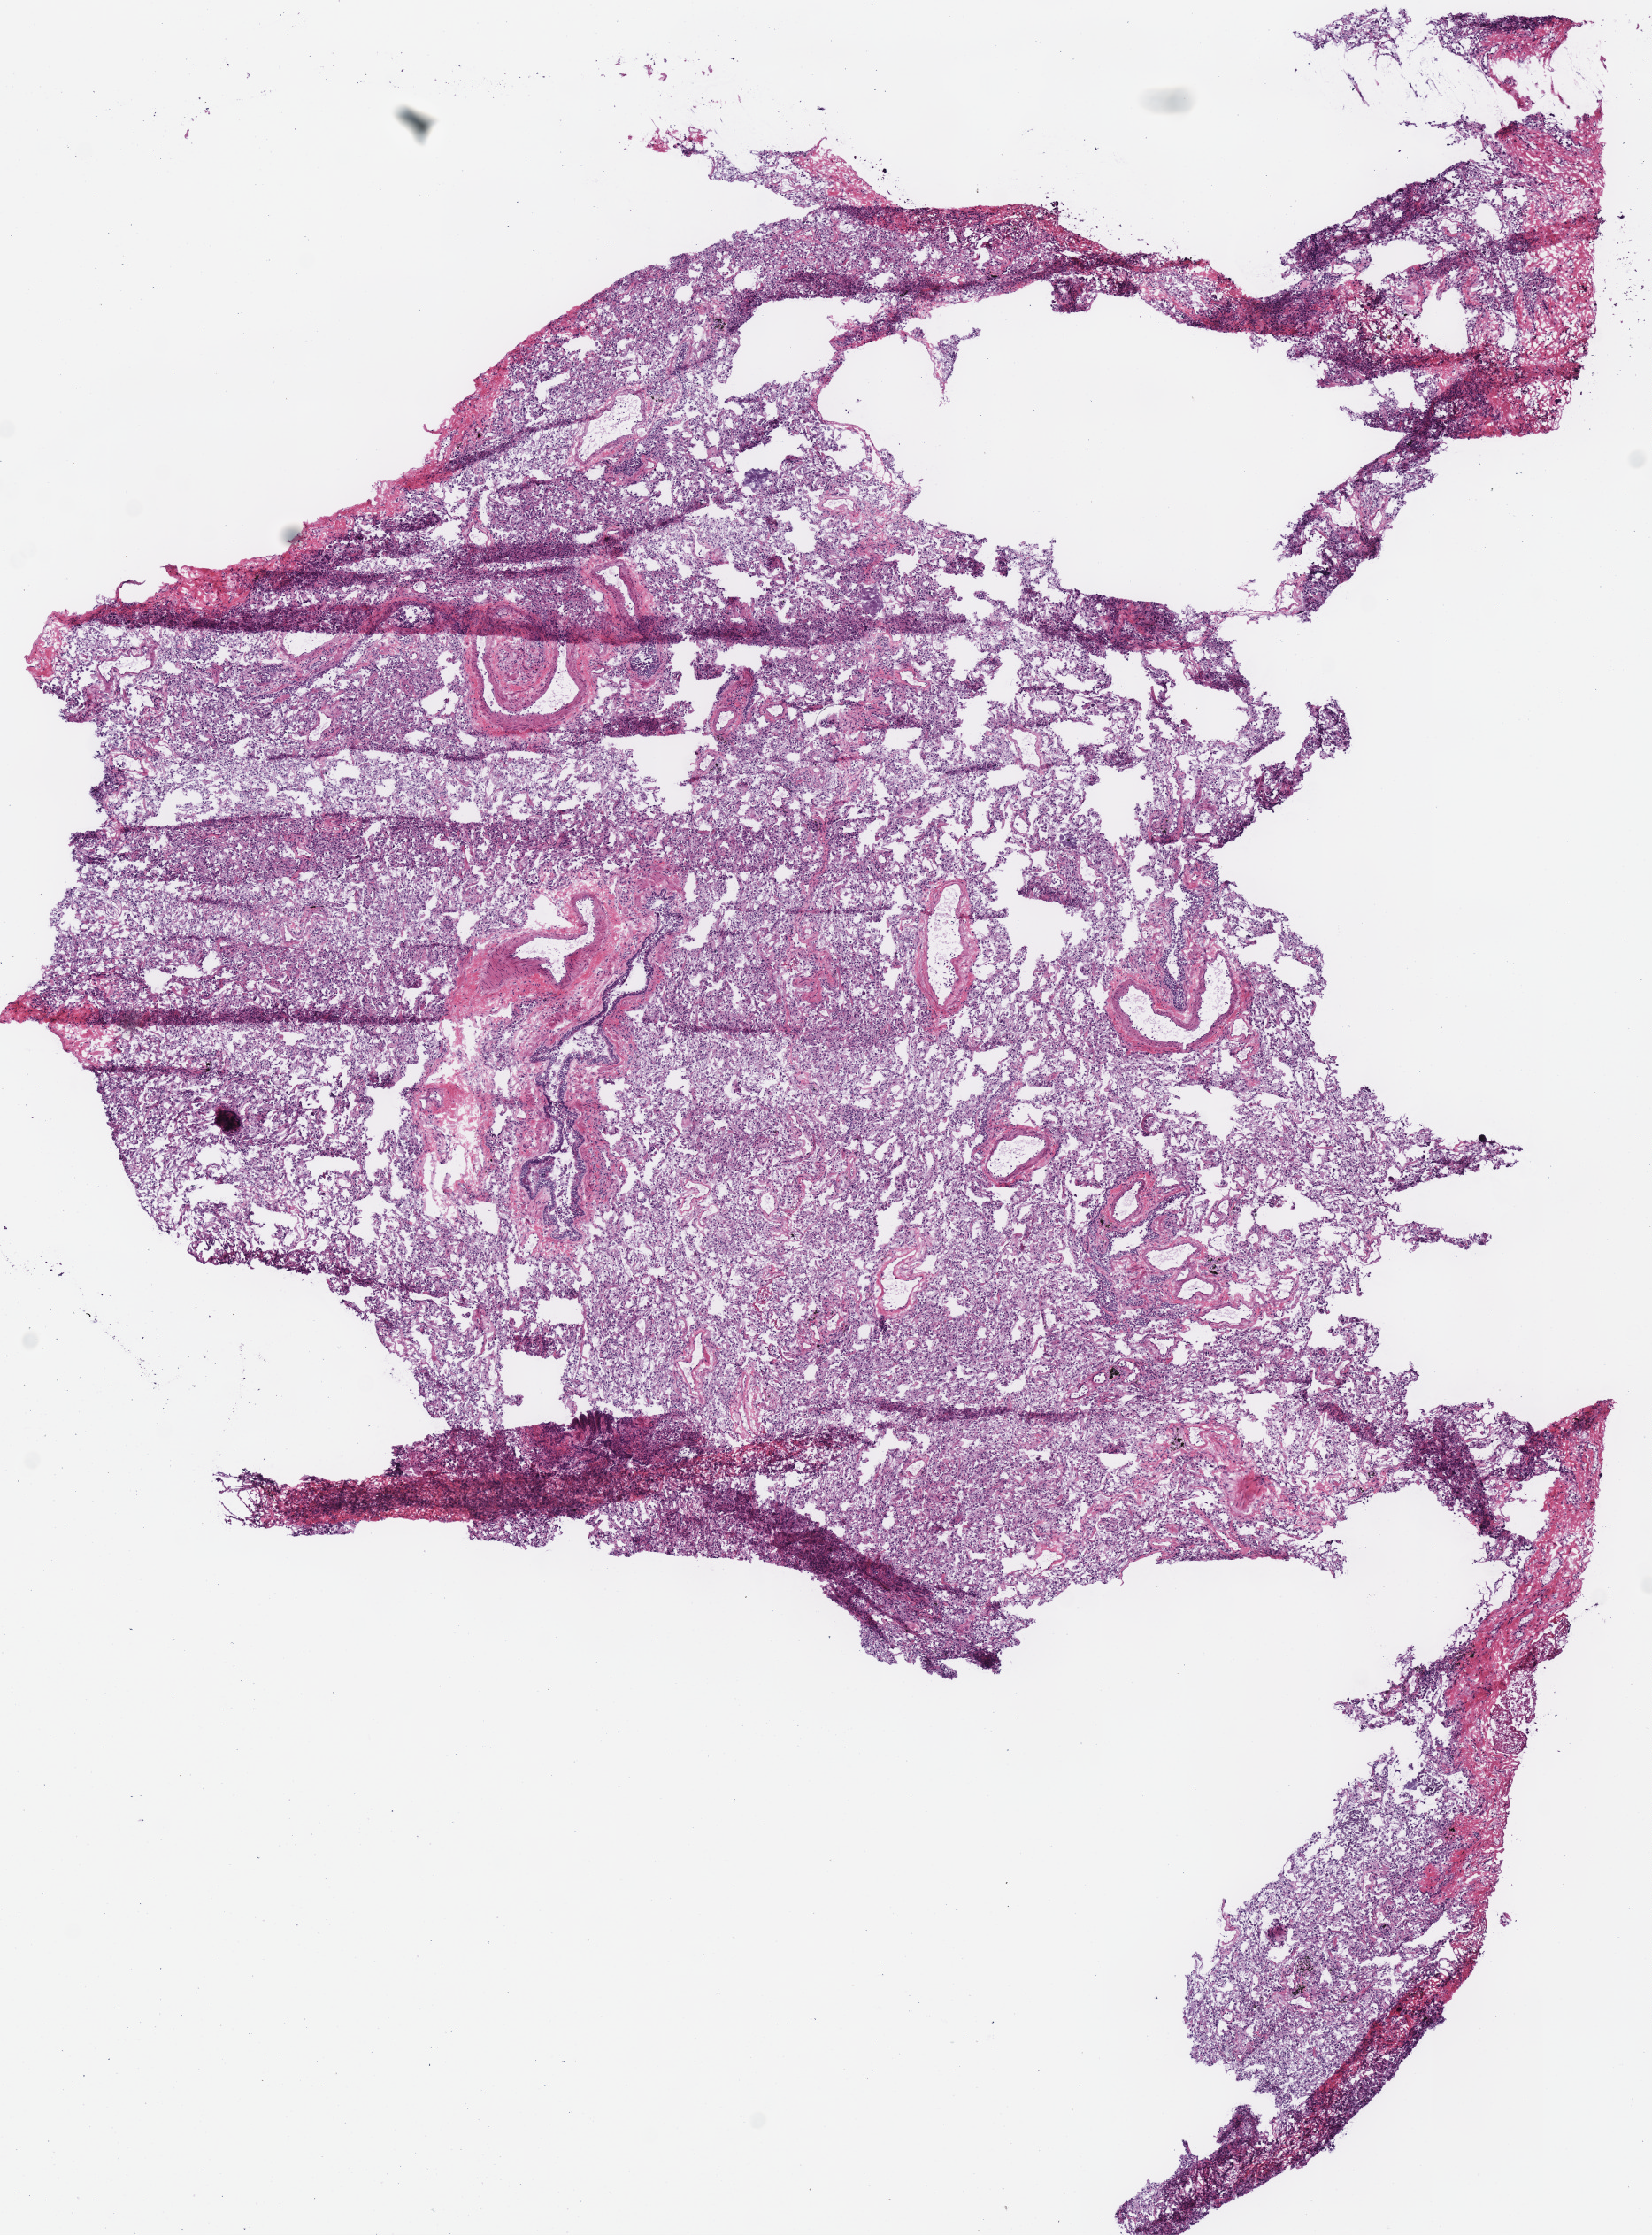
Digitized Hematoxylin and eosin (H&E) stained tissue section (whole slide) — shown as a low-resolution overview of the whole scanned area (about 7.3 x 9.9 mm, acquisition: 40x scan), frozen section from the top of the tissue portion, lung, solid tissue normal (non-tumour tissue) sample. Female, age 80 years at initial diagnosis.
This section: solid tissue normal sample (biorepository sample class). Patient diagnosis: Adenocarcinoma with mixed subtypes.